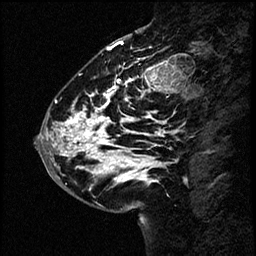
Breast MRI (dynamic contrast-enhanced), one sagittal slice. Slice 22 of 60 in the series (ordered by position). Dynamic contrast-enhanced study with each time point stored as its own series, time point 2 of 4 at this slice position (early post-contrast, ordered by acquisition time). 1.5 T. TE 4.2 ms, TR 17.6 ms. 256 × 256 image matrix. Female patient, age 43 years. Case-level facts recorded for this patient, not image findings: setting: breast cancer imaged before/during neoadjuvant chemotherapy.
Structures marked on this image (semi-automatic segmentation, software-assisted and operator-edited):
- analysis volume of interest (the breast-tissue region the enhancement analysis was run in; not a lesion): bounding box [x1, y1, x2, y2] px = [42, 57, 169, 191]
- tumour enhancement mask (voxels above the 100 % enhancement threshold inside the analysis volume of interest): [46, 69, 164, 183]